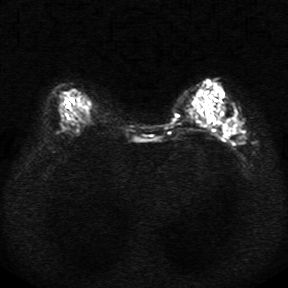
Breast MRI, one axial slice; position 12 of 34 along the scan axis; diffusion-weighted series; image 2 of 4 stored at this slice position (different b-values; order by instance number); 1.5 T; 5 mm slice thickness; 288 × 288 image matrix, field of view 340 × 340 mm. Female patient.
Annotated regions visible in this slice (expert manual segmentation):
- tumour on diffusion-weighted imaging: box from (x=223, y=117) to (x=241, y=133) px